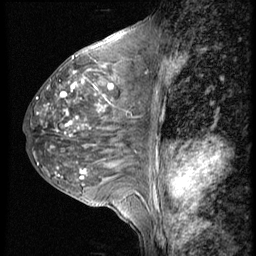
Breast MRI (dynamic contrast-enhanced), one sagittal slice; slice 25 of 56 in the series (ordered by position); 4 images stored at this slice position (order not interpretable as contrast timing); 1.5 T; TE 4.2 ms, TR 9 ms; 2.5 mm slice thickness; 256 × 256 image matrix. Patient: female, 50 years. Case-level facts recorded for this patient, not image findings: setting: breast cancer imaged before/during neoadjuvant chemotherapy; receptor status: triple-negative.
Annotated regions visible in this slice (semi-automatic segmentation, software-assisted and operator-edited):
- analysis volume of interest (the breast-tissue region the enhancement analysis was run in; not a lesion): bounding box (x1, y1, x2, y2) in pixels: (22, 46, 148, 188)
- tumour enhancement mask (voxels above the 140 % enhancement threshold inside the analysis volume of interest): (36, 72, 114, 174)